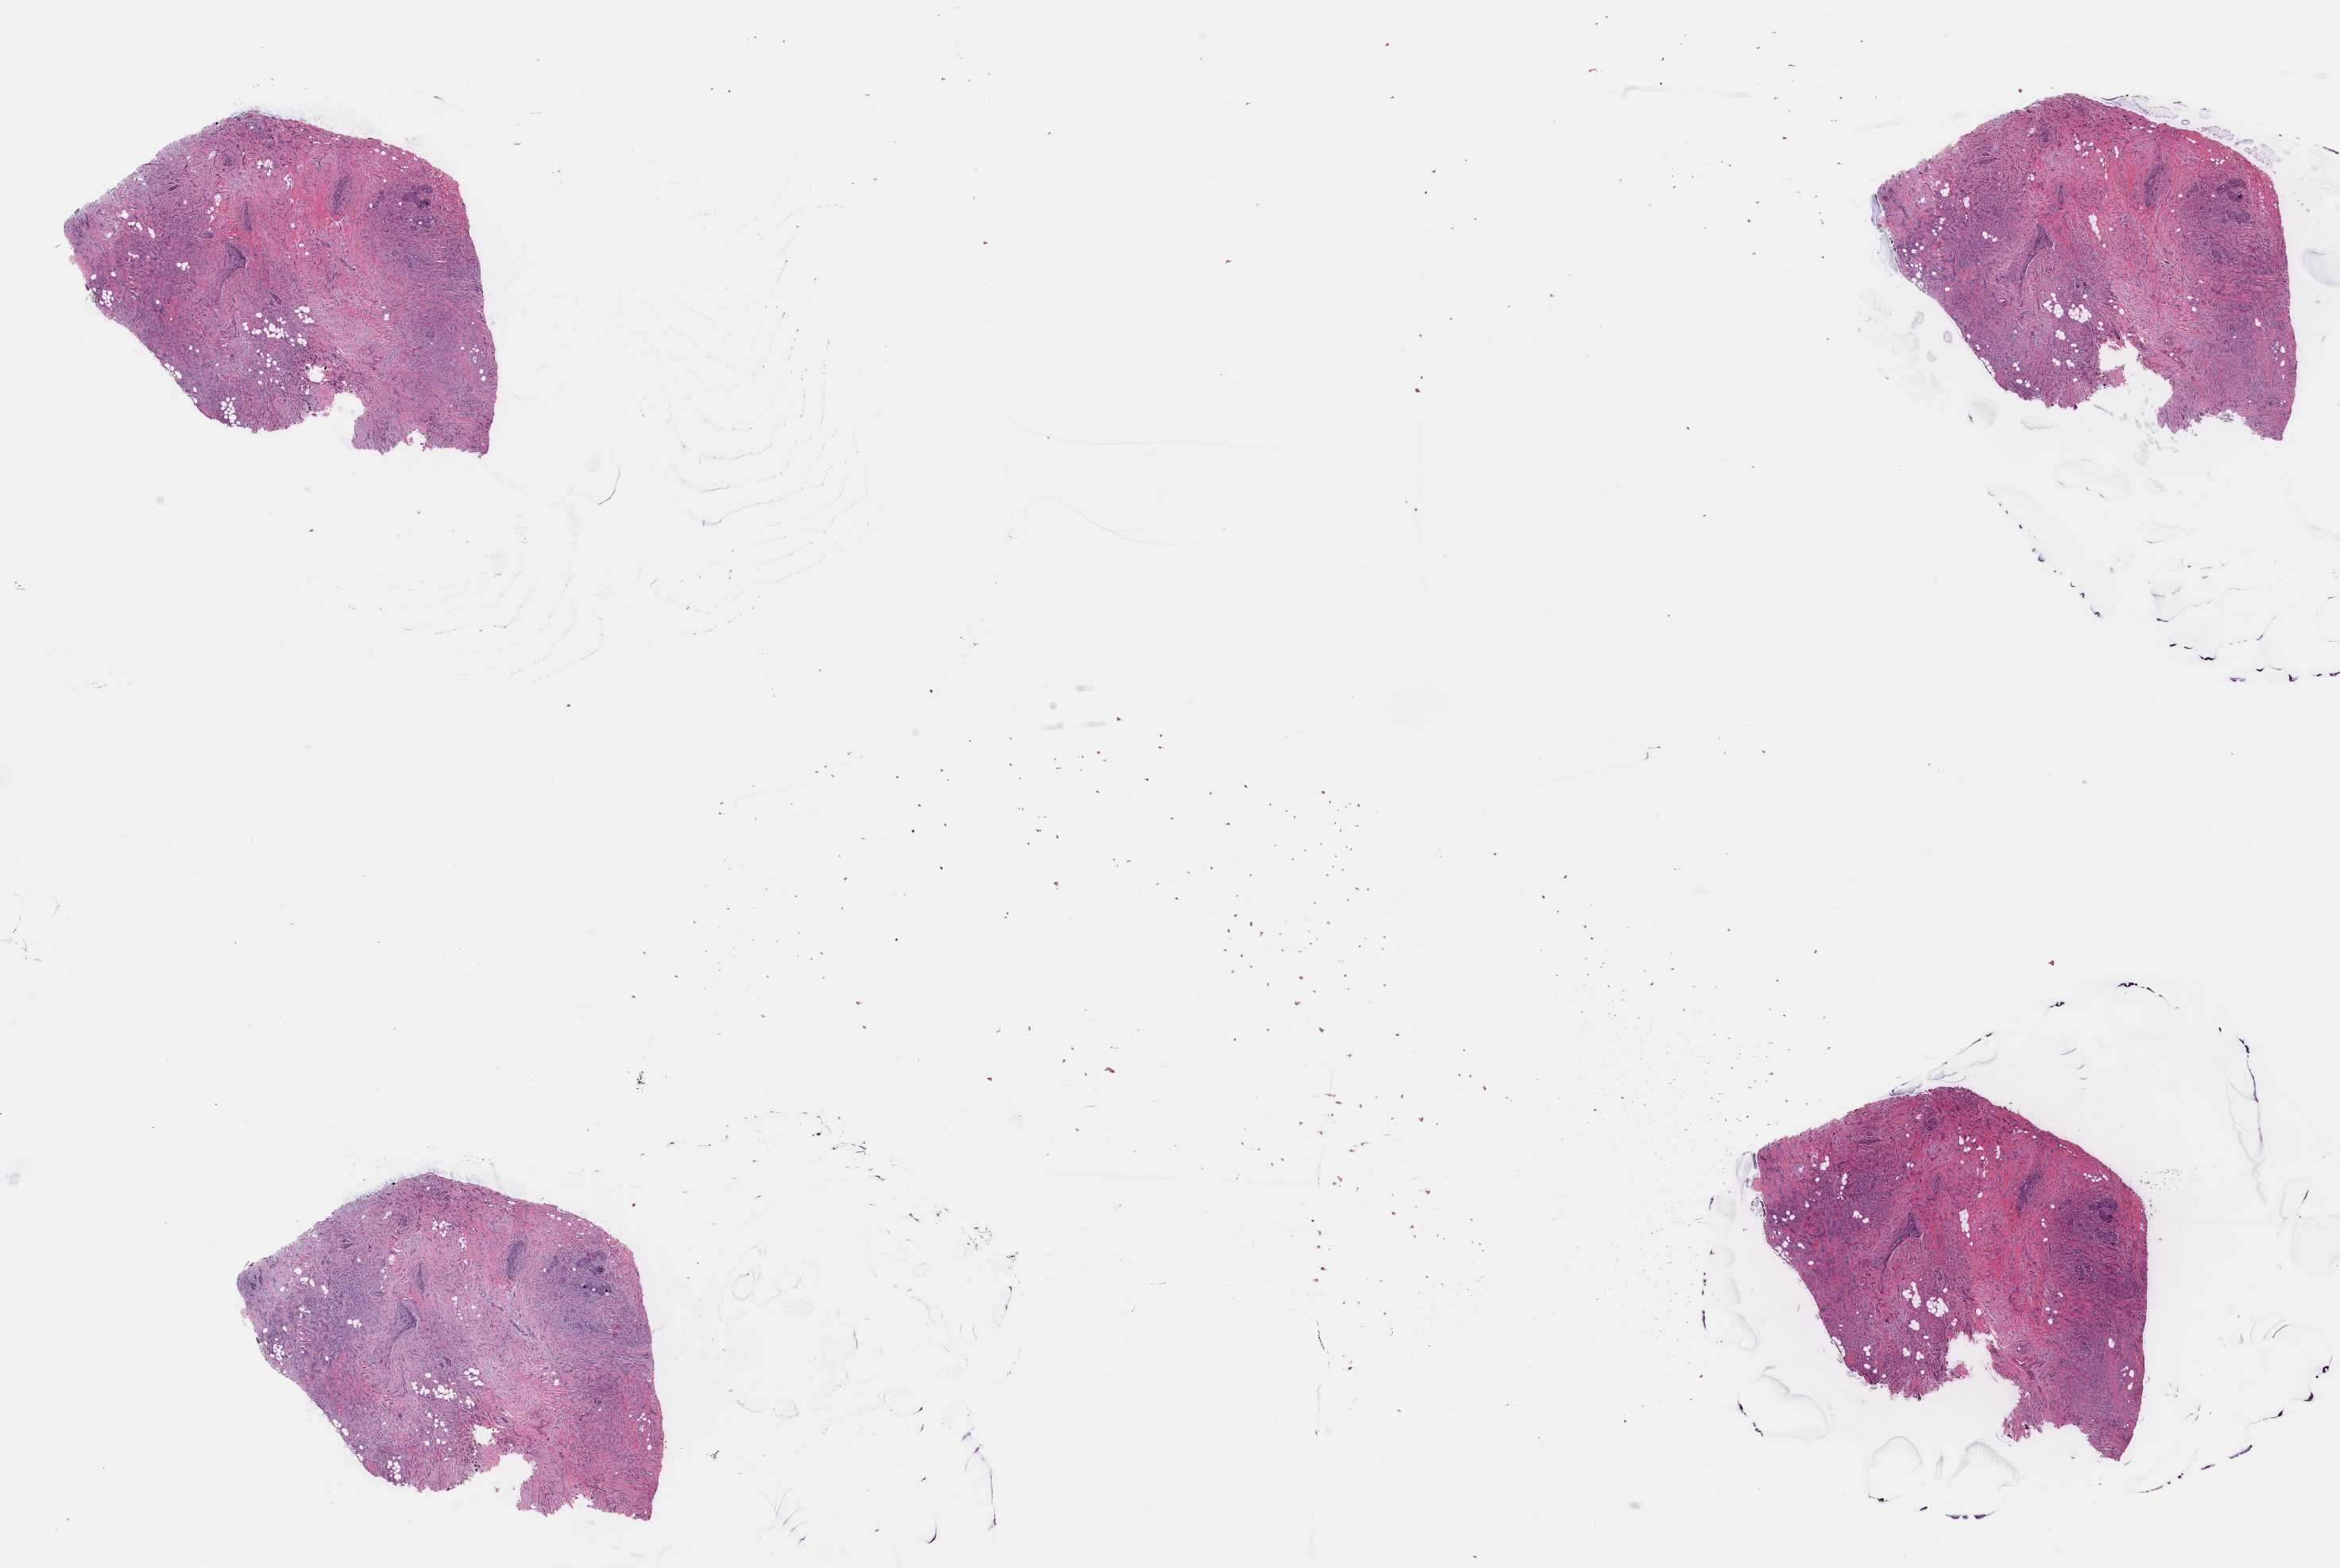
Whole-slide histology image, H&E, whole scanned area (about 23.2 x 15.6 mm) shown as a low-resolution overview. Formalin-fixed paraffin-embedded (FFPE) diagnostic section. Sample: primary tumour, breast. Patient: female, age at initial diagnosis 48 years.
TNM: T2 N3a M0. Lymph nodes positive (case pathology): 21 of 24 examined. AJCC pathologic stage: IIIC (7th edition). Diagnosis: Lobular carcinoma, NOS.